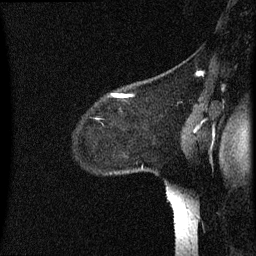
Breast MRI (dynamic contrast-enhanced), one sagittal slice; slice 52 of 60 in the series (ordered by position); dynamic contrast-enhanced series, image 2 of 3 at this slice position (ordered by acquisition); 1.5 T; TE 4.2 ms, TR 8.4 ms; 2.2 mm slice thickness; 256 × 256 image matrix, field of view 200 × 200 mm. Patient: female, 35 years. From the clinical record (not read from this slice): setting: breast cancer imaged before/during neoadjuvant chemotherapy; receptor status: HER2-positive.
Annotated regions visible in this slice (semi-automatic segmentation, software-assisted and operator-edited):
- analysis volume of interest (the breast-tissue region the enhancement analysis was run in; not a lesion): bounding box (x1, y1, x2, y2) in pixels: (97, 76, 164, 173)
- tumour enhancement mask (voxels above the 70 % enhancement threshold inside the analysis volume of interest): (112, 94, 125, 97)